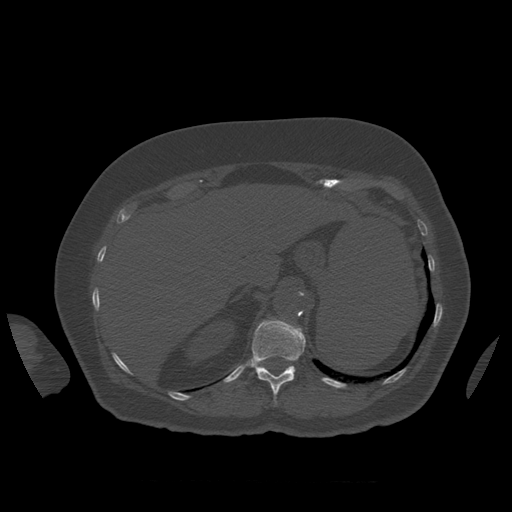
CT including the spine, one axial slice; slice 299 of 399 in the series (ordered by position); bone window (W 1800 / L 400 HU); 1.25 mm slice thickness; 512 × 512 image matrix, field of view 404 × 404 mm. Patient age 81 years. Case-level facts recorded for this patient, not image findings: primary cancer: renal.
Annotated regions visible in this slice (semi-automatic segmentation, software-assisted and operator-edited):
- L1 vertebra: box from (x=293, y=366) to (x=295, y=368) px
- T12 vertebra: (x=251, y=319)–(x=306, y=403)